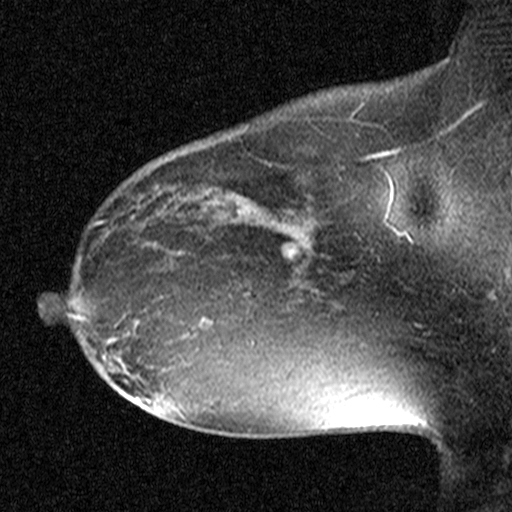
Breast MRI (dynamic contrast-enhanced), one sagittal slice; position 31 of 44 along the scan axis; dynamic contrast-enhanced study with each time point stored as its own series, time point 2 of 3 at this slice position (early post-contrast, ordered by acquisition time); 1.5 T; TE 4.5 ms, TR 11 ms; 3 mm slice thickness; 512 × 512 image matrix, field of view 200 × 200 mm. Patient: female, 38 years. Case-level facts recorded for this patient, not image findings: setting: breast cancer imaged before/during neoadjuvant chemotherapy; receptor status: HR-positive, HER2-negative.
Outlined on this slice (semi-automatically segmented with operator editing):
- analysis volume of interest (the breast-tissue region the enhancement analysis was run in; not a lesion): bounding box (x1, y1, x2, y2) in pixels: (182, 232, 291, 349)
- tumour enhancement mask (voxels above the 90 % enhancement threshold inside the analysis volume of interest): (203, 273, 233, 320)